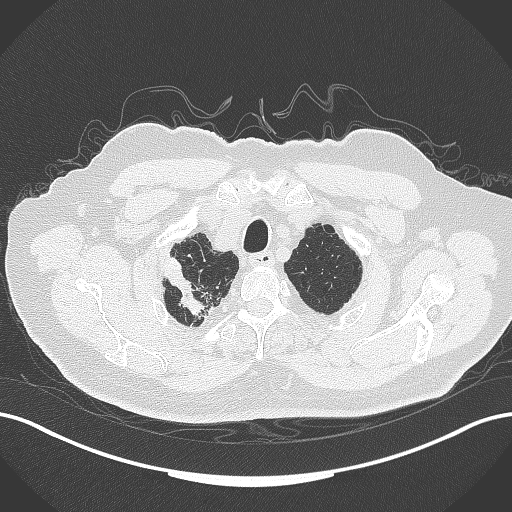
Chest CT, one axial slice. Position 323 of 389 along the scan axis. Reconstruction kernel B70f. 120 kVp. Lung window (W 1500 / L -600 HU). 1 mm slice thickness. 512 × 512 image matrix. Male patient, age 72 years. Case-level facts recorded for this patient, not image findings: clinical TNM (as recorded): T1a N0 M0.
Annotated regions visible in this slice (bounding box drawn by a radiologist):
- lung tumour (recorded histology: squamous cell carcinoma): bounding box <162,250,207,315> (left, top, right, bottom; pixels)